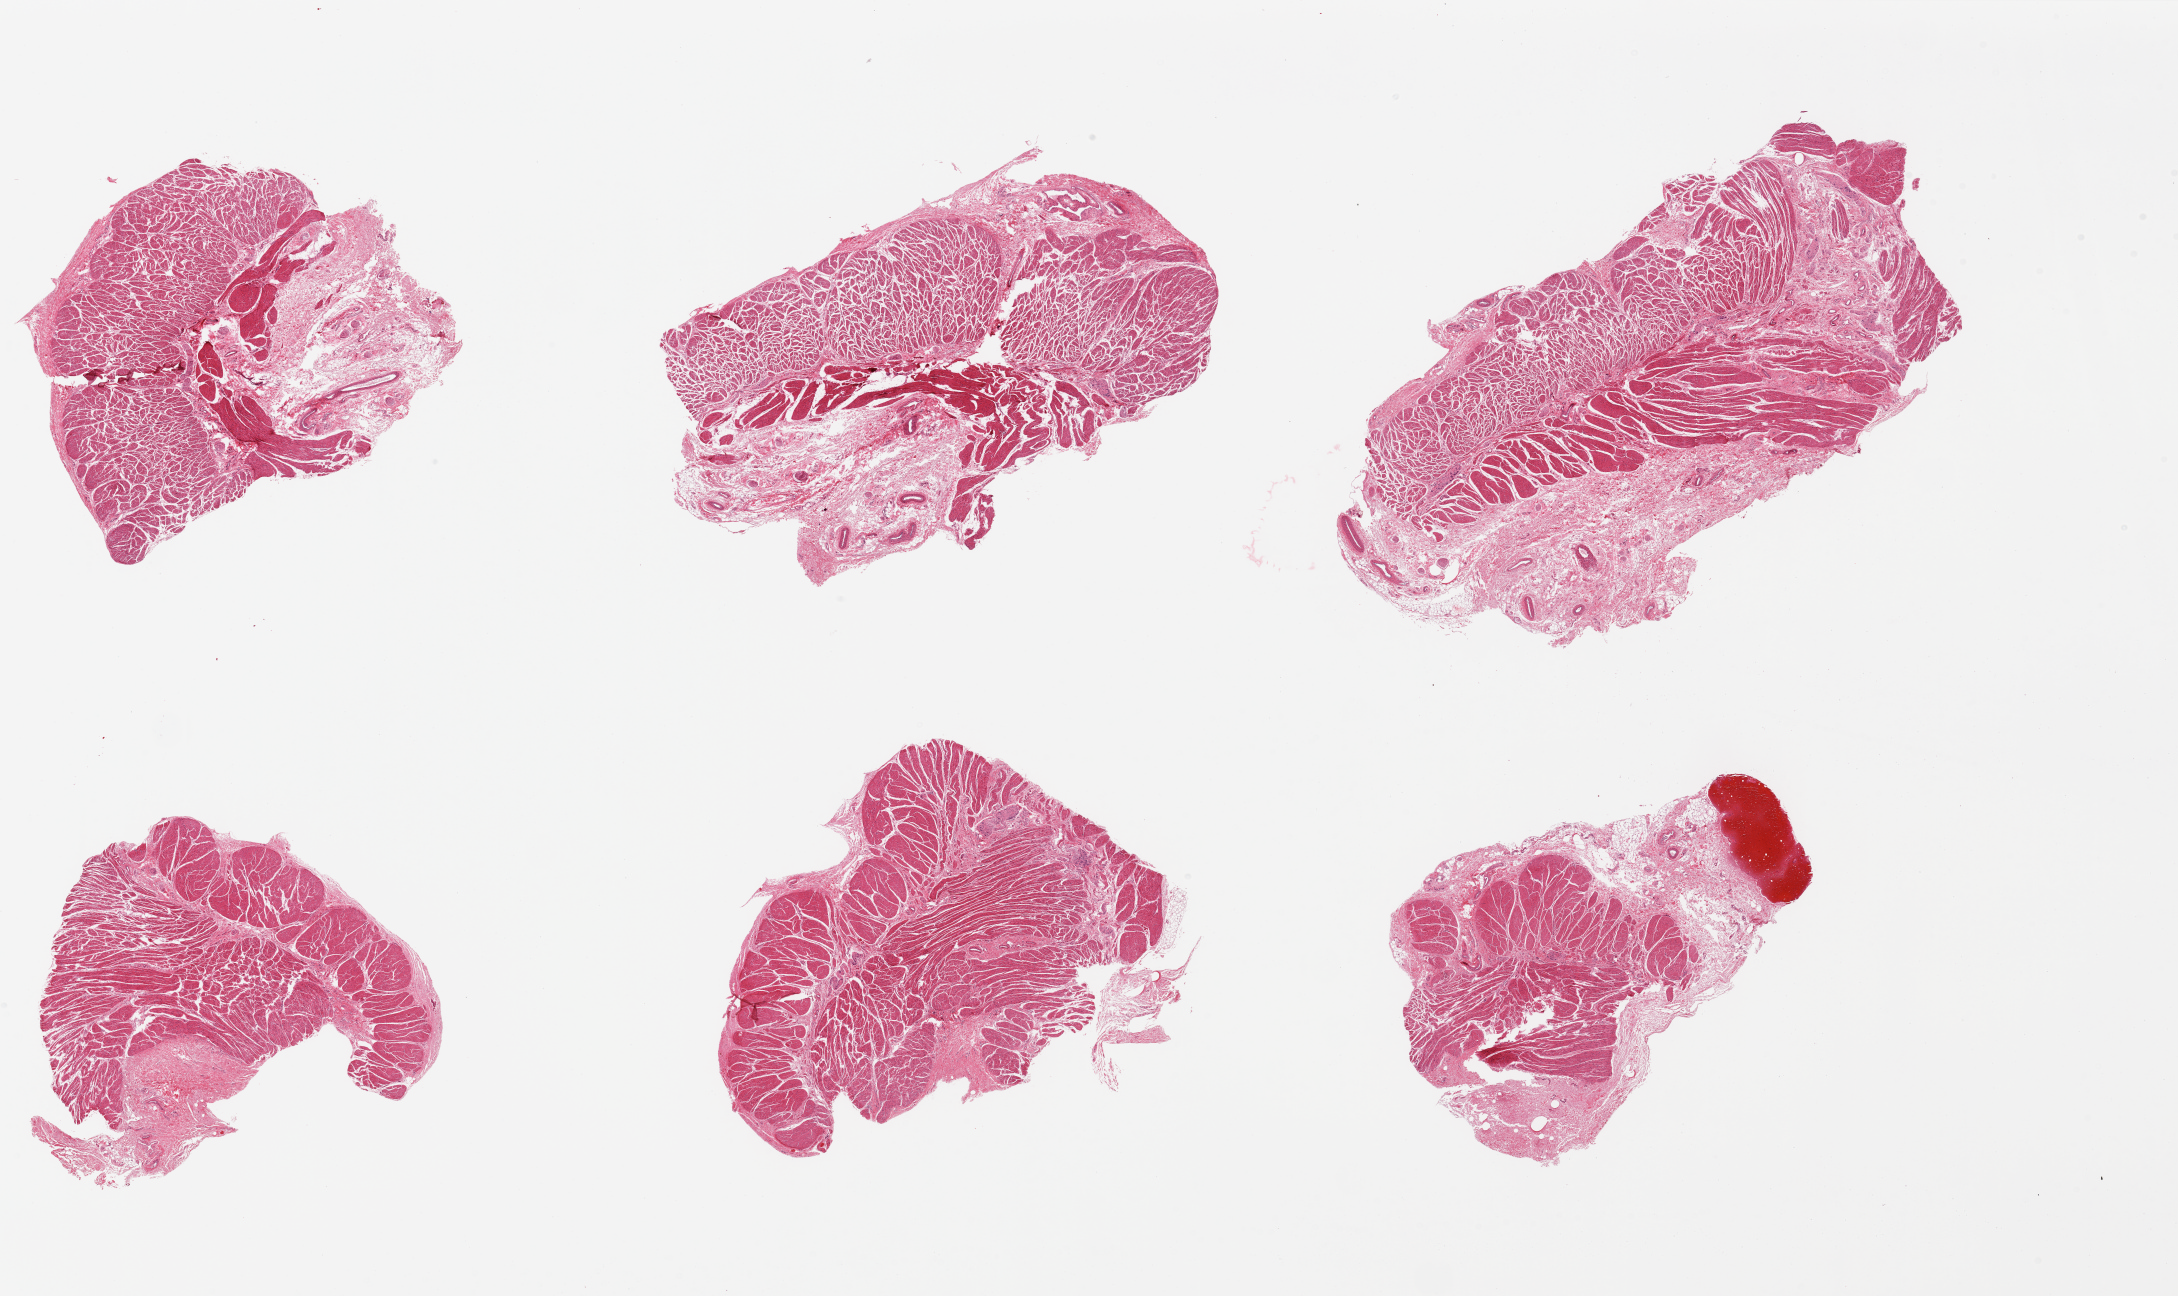
Whole-slide image, hematoxylin and eosin (H&E) stain, shown as a low-resolution overview of the whole scanned area (about 34.5 x 20.5 mm, acquisition: 20x scan), PAXgene-fixed, paraffin-embedded tissue, sampled site (target tissue): esophageal muscle, tissue donor sample. Male donor.
Pathologist's review note for this sample: 6 pieces, all muscularis, adherent nubbins of fat on most.